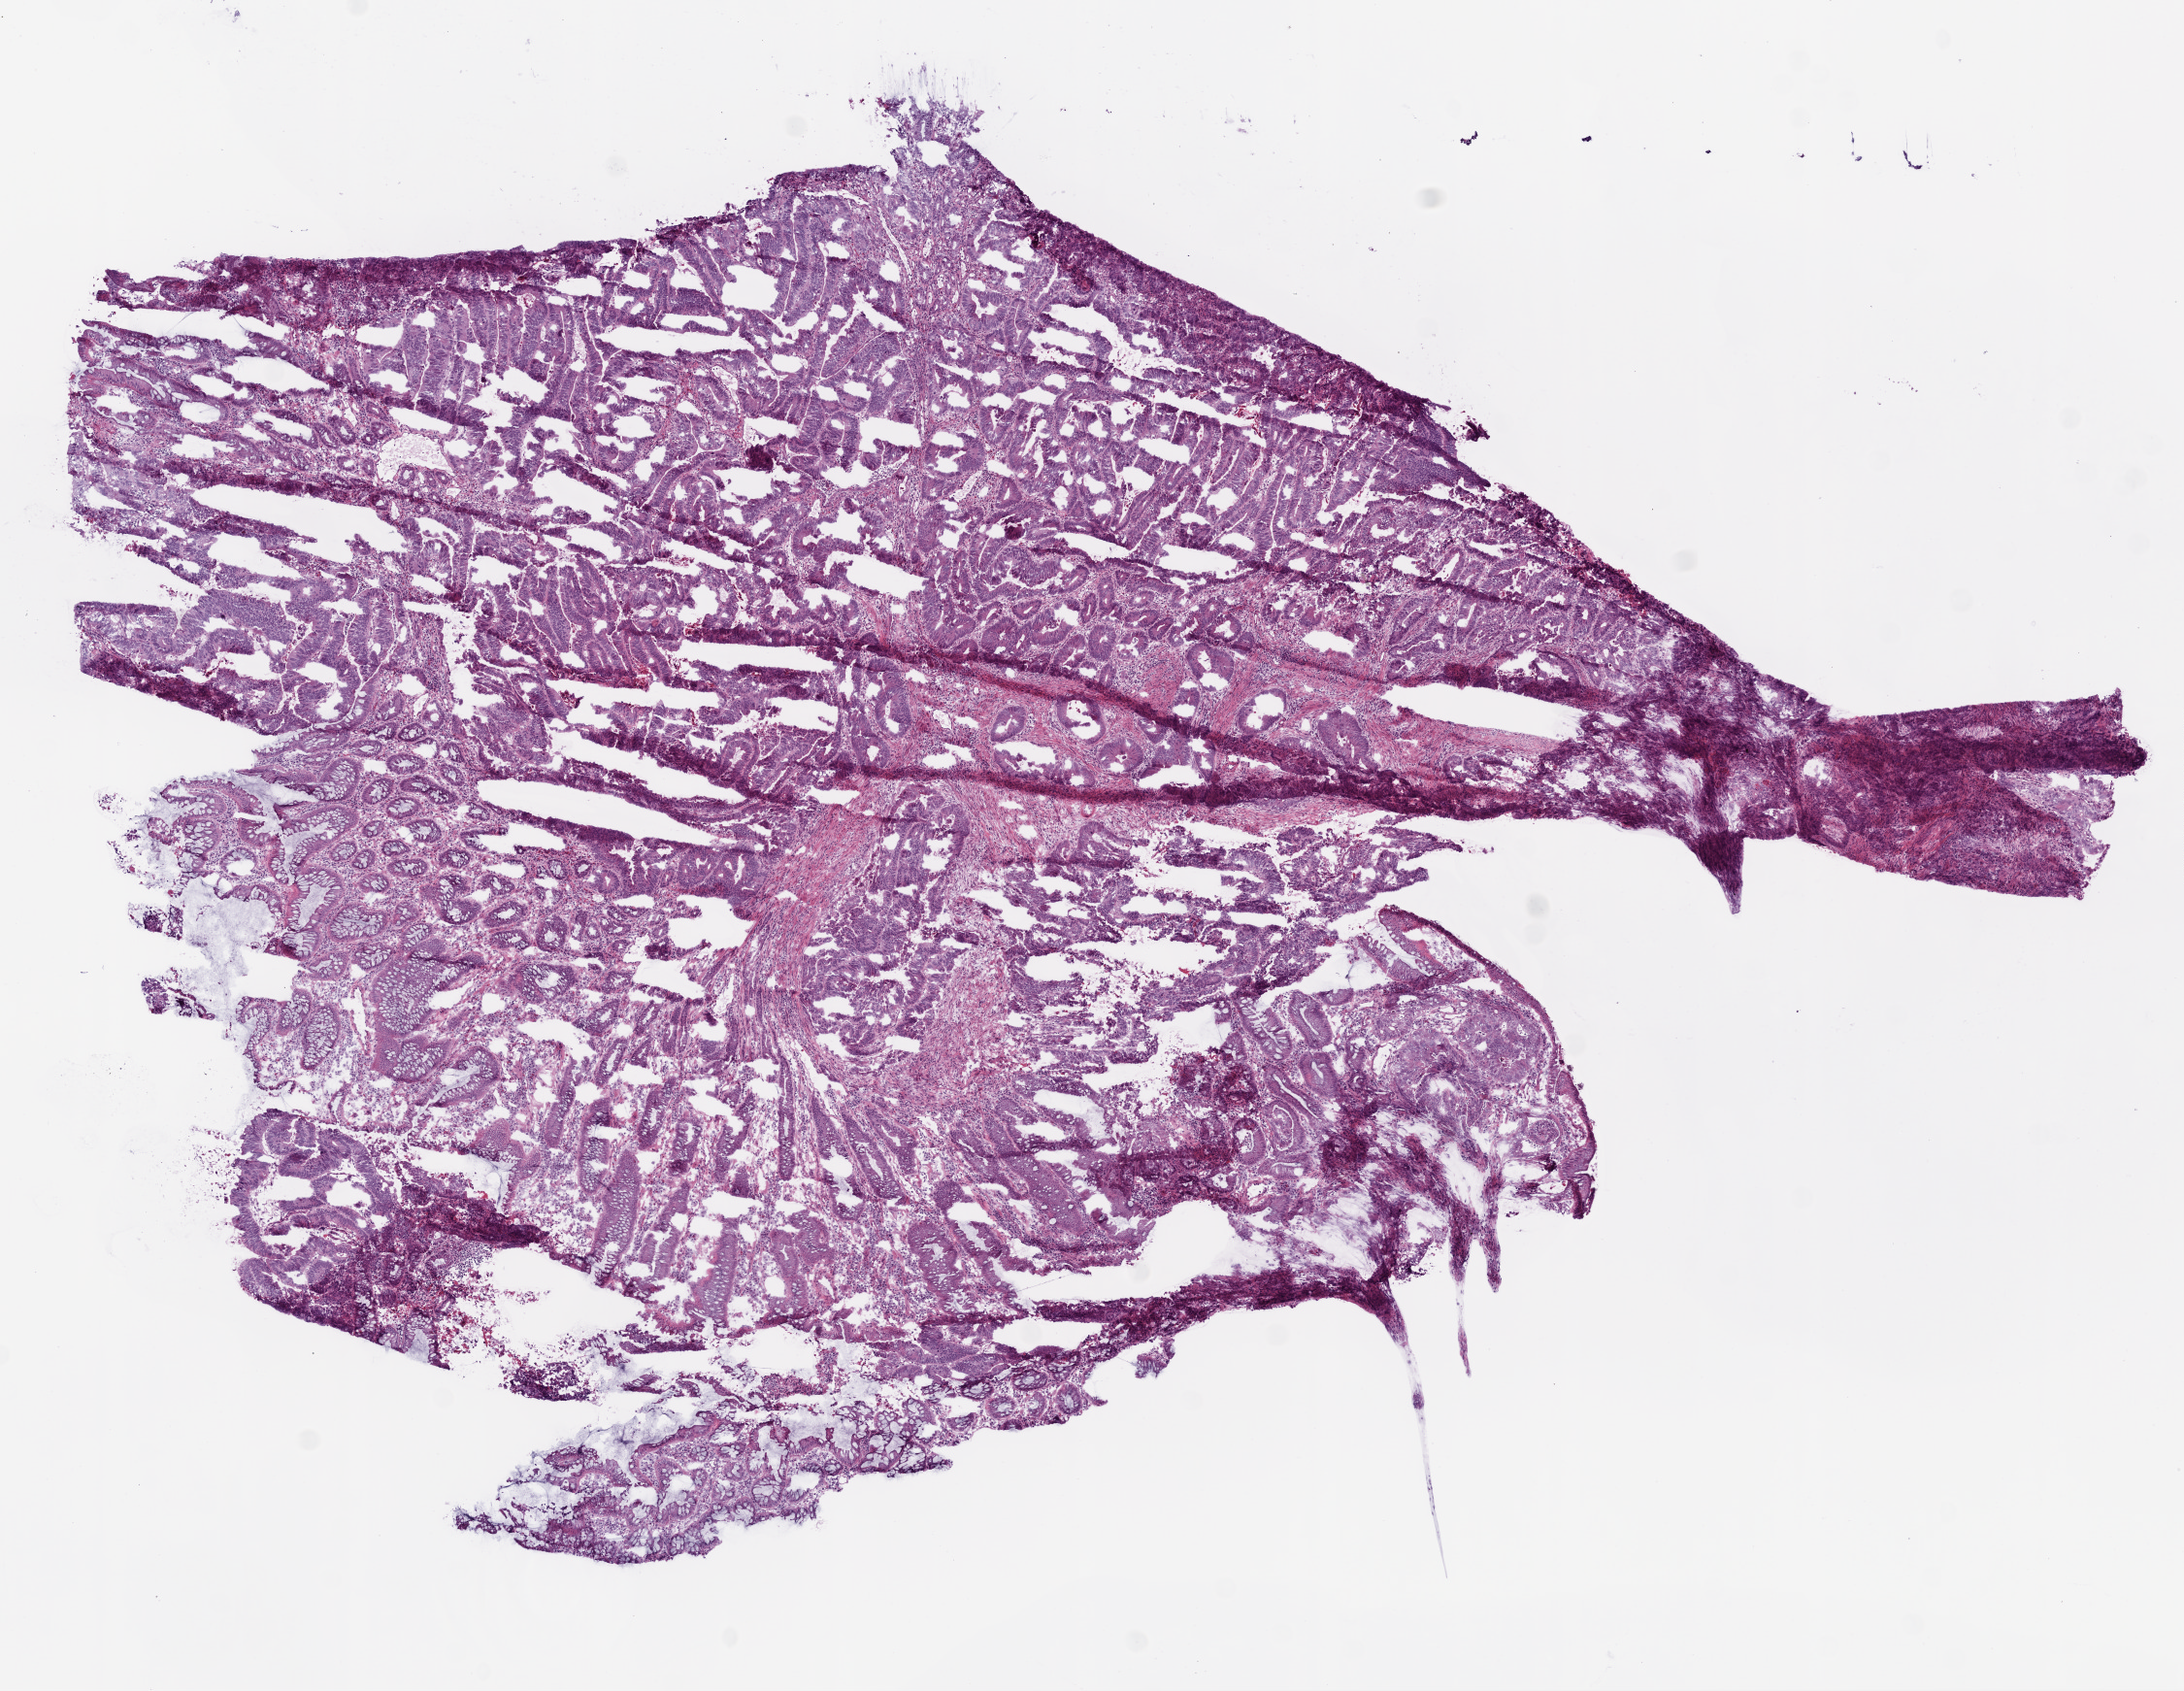
Whole-slide histology image, H&E-stained — a low-resolution overview of the entire scanned area, about 9.0 x 7.0 mm, frozen section from the top of the tissue portion, rectum, primary tumour sample. Male, age 63 years at initial diagnosis. Pathologist review of this section (percent, as recorded): tumour cells 75%, tumour nuclei 75%, normal cells 10%, stromal cells 10%, necrosis 5%.
AJCC pathologic stage: I (6th edition). Lymph nodes positive (case pathology): 0 of 33 examined. Histologic diagnosis: Adenocarcinoma, NOS.